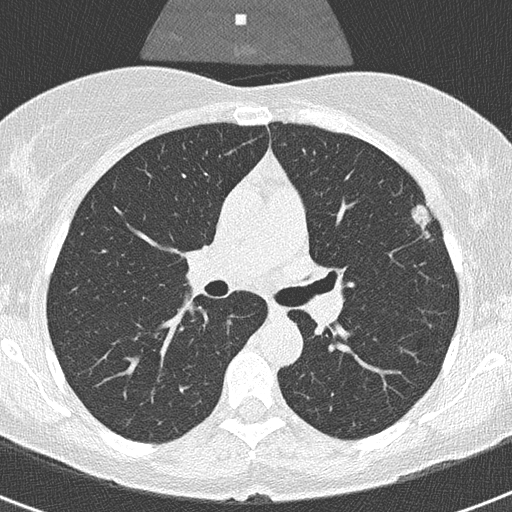
Low-dose screening chest CT, one axial slice. Position 204 of 320 along the scan axis. 120 kVp. Lung window (W 1500 / L -600 HU). 2 mm slice thickness. 512 × 512 image matrix, field of view 290 × 290 mm.
Outlined on this slice (outlined manually by an expert reader):
- lesion 1 (tumor, upper lobe of left lung): box from (x=412, y=203) to (x=431, y=238) px